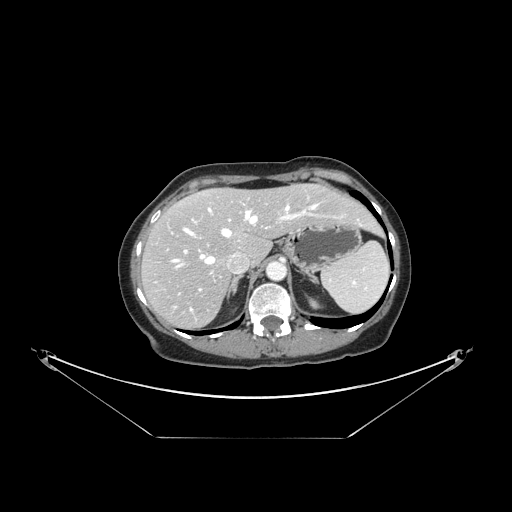
Contrast-enhanced abdominal CT, one axial slice. Position 109 of 148 along the scan axis. Reconstruction kernel STANDARD. 120 kVp. Intravenous contrast given. Soft-tissue window (W 400 / L 40 HU). 512 × 512 image matrix, field of view 500 × 500 mm. Female patient, age 73 years. From the clinical record (not read from this slice): diagnosis: colorectal cancer liver metastases, imaged before liver resection; multiple liver metastases: no; largest metastasis: 1 cm; chemotherapy before resection: yes.
Annotated regions visible in this slice (manually delineated by an expert):
- hepatic veins: bounding box (x1, y1, x2, y2) in pixels: (173, 203, 359, 311)
- liver: (143, 185, 378, 328)
- planned liver remnant (the part of the liver to remain after resection): (168, 184, 378, 261)
- portal vein (with intrahepatic branches): (184, 209, 309, 291)